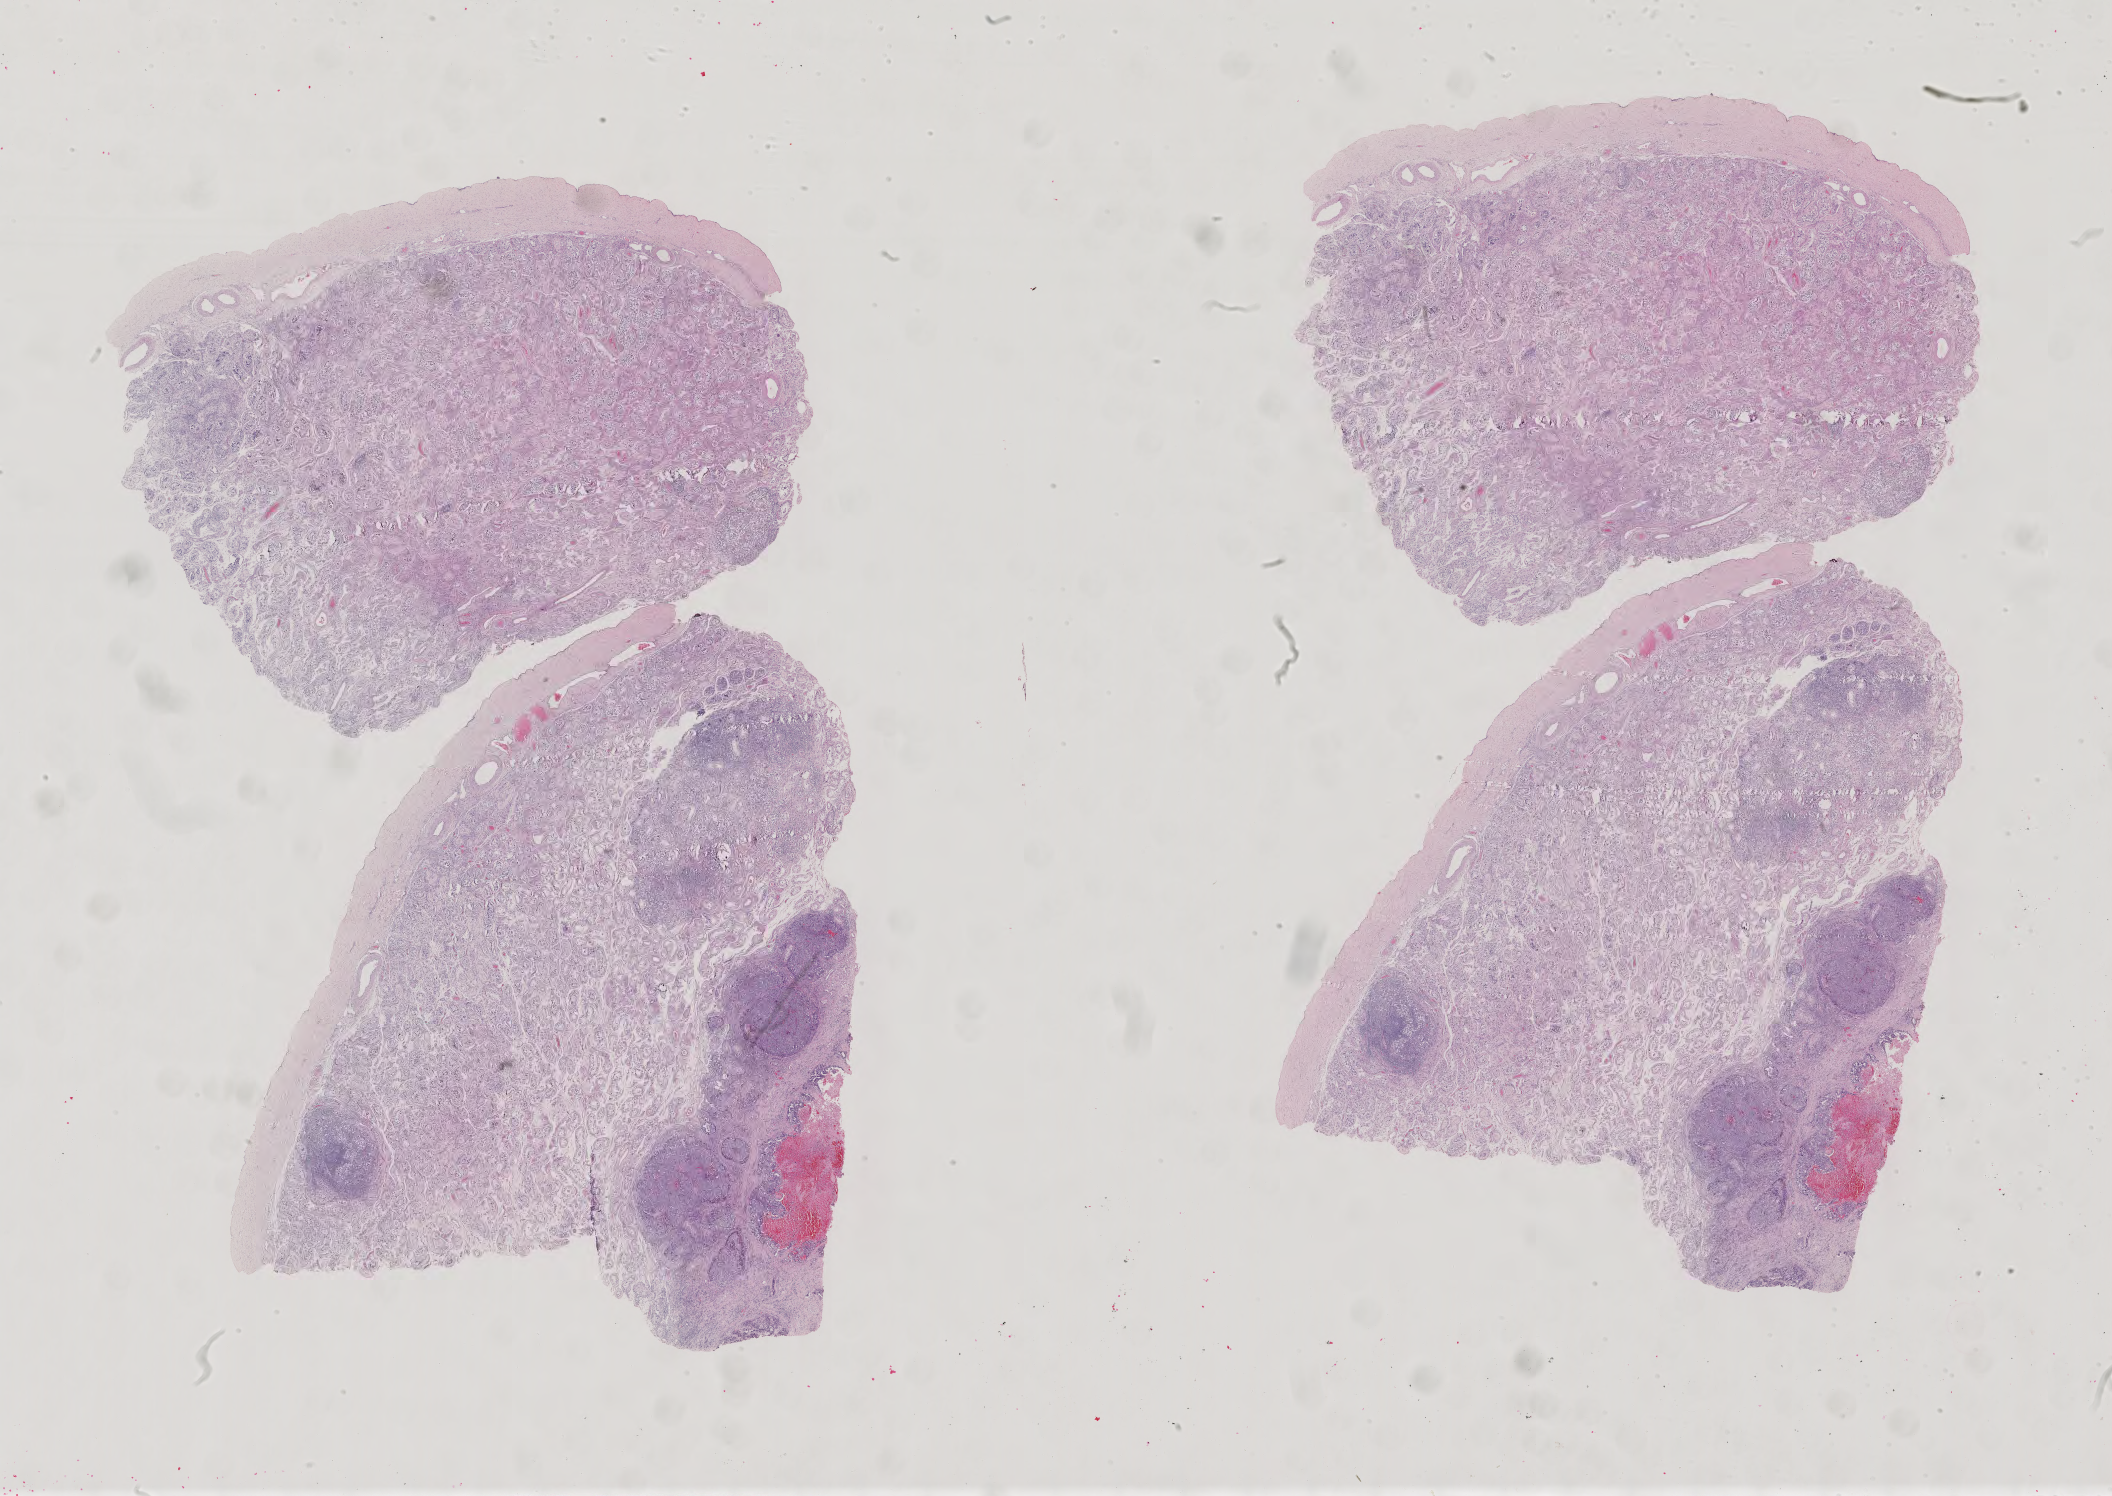
Whole-slide histology image, H&E, shown as a low-resolution overview of the whole scanned area (about 30.8 x 21.8 mm), FFPE section, sample: primary tumour, testis. Male patient; age at initial diagnosis 21 years.
Histologic diagnosis: Embryonal carcinoma, NOS. TNM: T2 N0 M0. AJCC pathologic stage: IB (6th edition). Laterality: right.